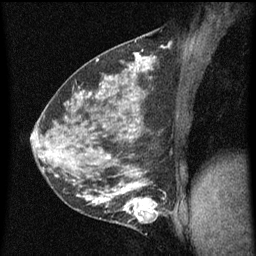
Breast MRI (dynamic contrast-enhanced), one sagittal slice; slice 30 of 60 in the series (ordered by position); dynamic contrast-enhanced series, image 2 of 5 at this slice position (ordered by acquisition); 1.5 T; TE 4.2 ms, TR 8 ms; 2 mm slice thickness; 256 × 256 image matrix. Patient: female, 35 years.
Annotated regions visible in this slice (semi-automatic segmentation, software-assisted and operator-edited):
- analysis volume of interest (the breast-tissue region the enhancement analysis was run in; not a lesion): bounding box (x1, y1, x2, y2) in pixels: (118, 190, 165, 229)
- tumour enhancement mask (voxels above the 70 % enhancement threshold inside the analysis volume of interest): (118, 190, 165, 223)